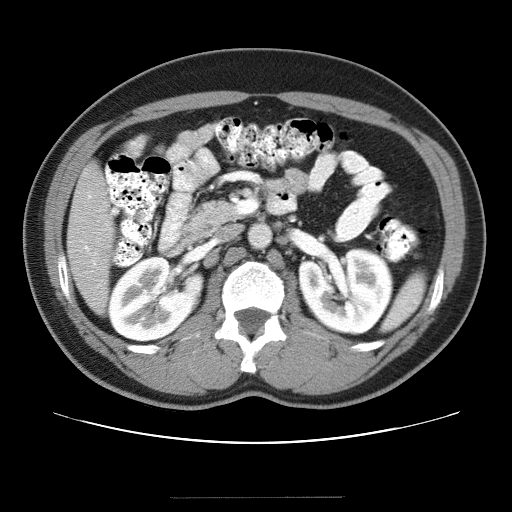
Contrast-enhanced abdominal CT (liver protocol), one axial slice. Slice 9 of 40 in the series (ordered by position). Reconstruction kernel STANDARD. 120 kVp. Soft-tissue window (W 400 / L 40 HU). 5 mm slice thickness. 512 × 512 image matrix, field of view 380 × 380 mm. From the clinical record (not read from this slice): diagnosis: hepatocellular carcinoma (patient treated with transarterial chemoembolisation; whether this scan precedes or follows treatment is not stated here); TNM stage (as recorded): Stage-IVA; Child-Pugh class: B; tumour nodularity: multinodular.
Structures marked on this image (semi-automatic segmentation, software-assisted and operator-edited):
- liver parenchyma outside the tumour (the mass and vessels are separate outlines, so this box may not span the whole liver): bounding box <66,162,114,312> (left, top, right, bottom; pixels)
- liver vessels: <80,195,108,266>